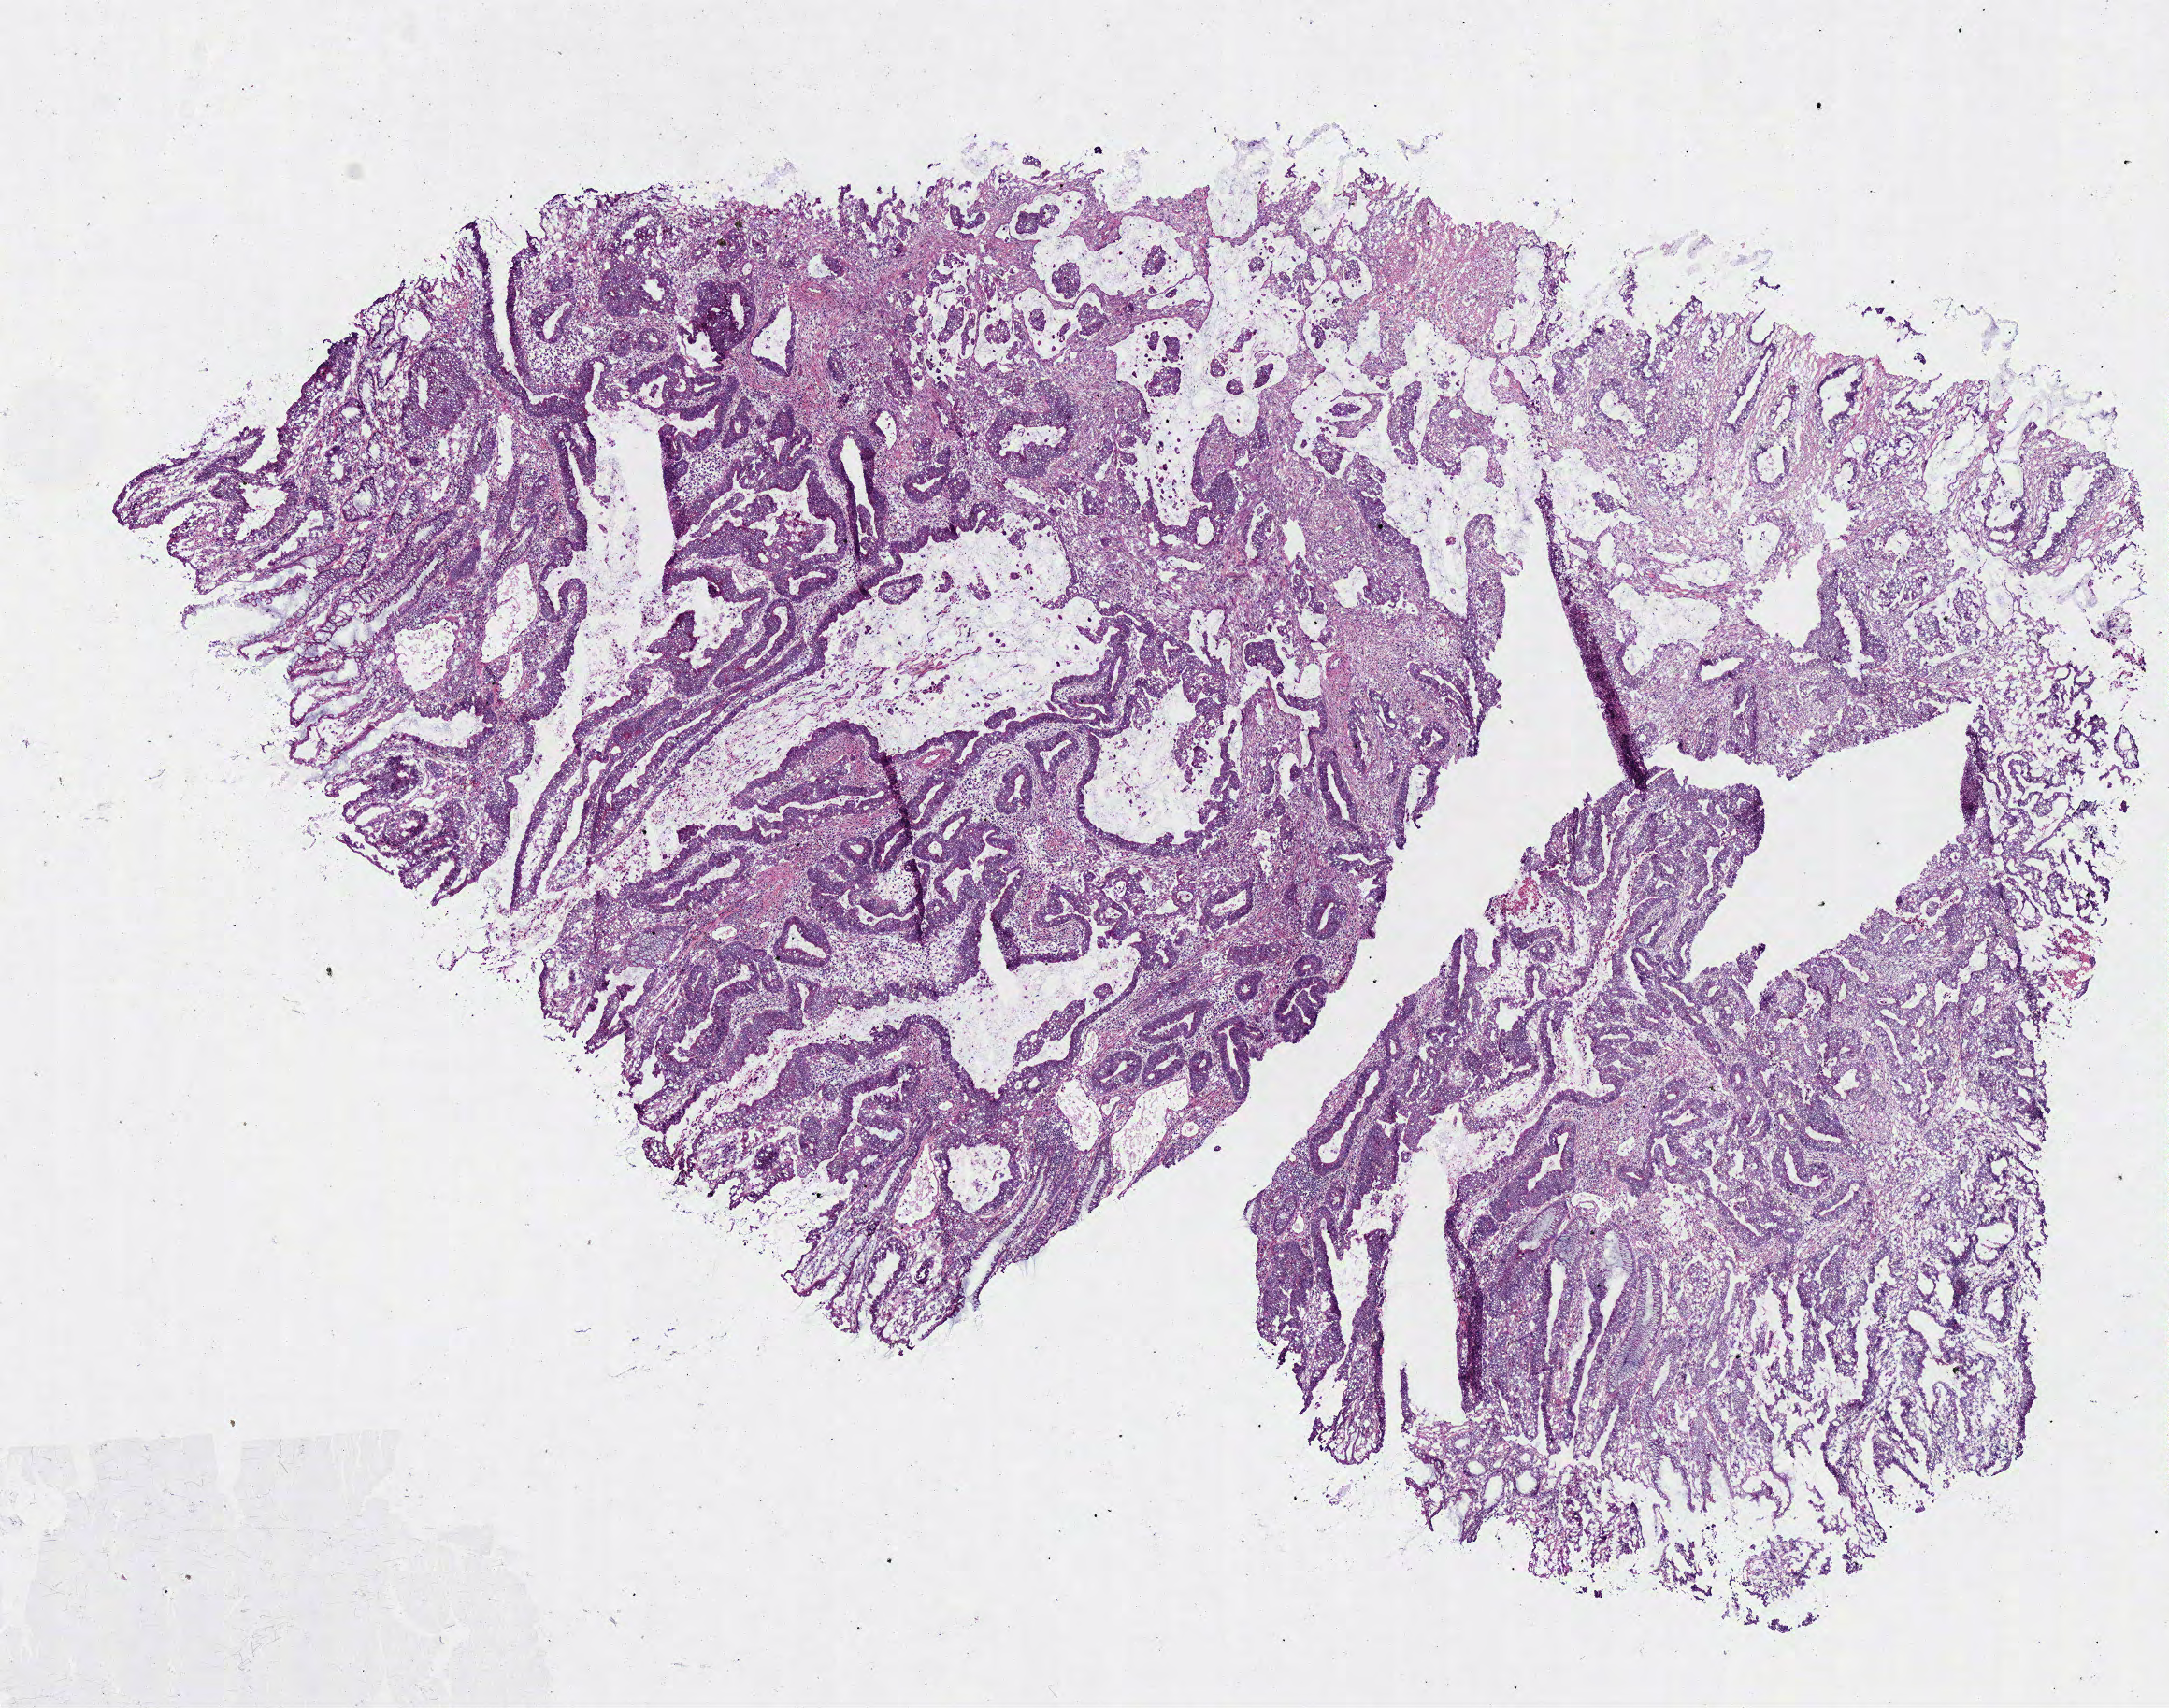
Digitized H&E tissue section (whole slide), whole scanned area (about 9.1 x 7.2 mm) shown as a low-resolution overview; frozen section from the bottom of the tissue portion; sample: primary tumour, rectum. Female patient; age at initial diagnosis 72 years. Slide review estimates, as recorded: tumour cells 93%, tumour nuclei 80%, normal cells 5%, necrosis 2%. Infiltration values recorded for this section: lymphocyte infiltration 12%, neutrophil infiltration 2%.
* AJCC pathologic stage: IIA (7th edition)
* pathologic diagnosis: Adenocarcinoma, NOS (rectosigmoid junction)